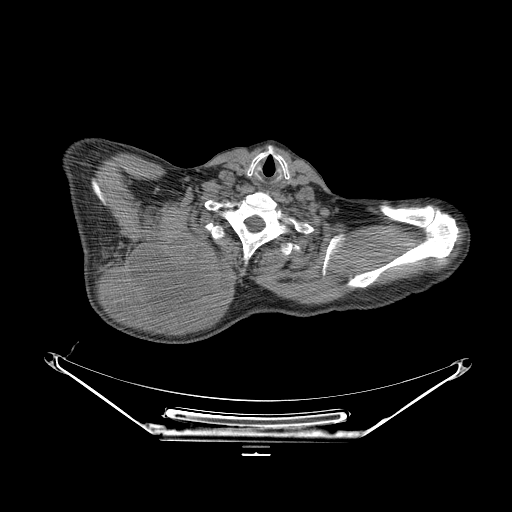
CT of an extremity soft-tissue mass (from a PET/CT study), one axial slice; slice 211 of 267 in the series (ordered by position); reconstruction kernel STANDARD; 140 kVp; soft-tissue window (W 400 / L 40 HU); 3.75 mm slice thickness; 512 × 512 image matrix, field of view 500 × 500 mm. Male patient. Case-level facts recorded for this patient, not image findings: histological type: pleiomorphic spindle cell undifferentiated; grade: high; site of the primary tumour: right parascapusular.
Annotated regions visible in this slice (expert contour drawn on MRI and transferred to this co-registered scan by the dataset authors):
- gross tumour volume including surrounding oedema: bounding box <98,228,236,325> (left, top, right, bottom; pixels)
- gross tumour volume (mass): <103,235,218,321>